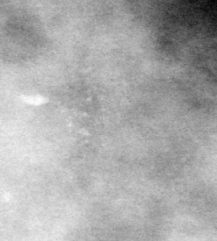
Crop from a digitized film mammogram around one marked abnormality, left breast, CC view.
- Finding: calcifications, morphology pleomorphic, distribution clustered; BI-RADS assessment category 4; subtlety rating 2 on a 1 (subtle) to 5 (obvious) scale; pathology result (as recorded, not read from the image): malignant.